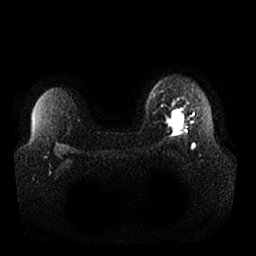
Breast MRI, one axial slice; slice 23 of 32 in the series (ordered by position); diffusion-weighted series; image 2 of 4 stored at this slice position (different b-values; order by instance number); 1.5 T; 256 × 256 image matrix. Female patient.
Structures marked on this image (expert manual segmentation):
- tumour on diffusion-weighted imaging: bounding box [x1, y1, x2, y2] px = [170, 109, 184, 130]